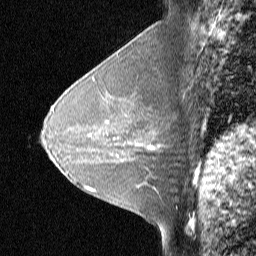
Breast MRI (dynamic contrast-enhanced), one sagittal slice; slice 28 of 48 in the series (ordered by position); dynamic contrast-enhanced study with each time point stored as its own series, time point 2 of 3 at this slice position (early post-contrast, ordered by acquisition time); 1.5 T; TE 4 ms, TR 30 ms; 3 mm slice thickness; 256 × 256 image matrix. Patient: female, 31 years. From the clinical record (not read from this slice): setting: breast cancer imaged before/during neoadjuvant chemotherapy; receptor status: HER2-positive.
Annotated regions visible in this slice (semi-automatically segmented with operator editing):
- analysis volume of interest (the breast-tissue region the enhancement analysis was run in; not a lesion): box from (x=129, y=130) to (x=175, y=167) px
- tumour enhancement mask (voxels above the 90 % enhancement threshold inside the analysis volume of interest): (x=147, y=145)–(x=159, y=150)